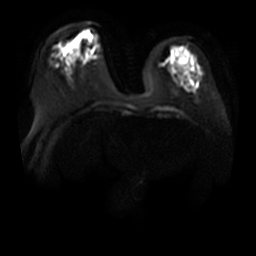
Breast MRI, one axial slice; position 13 of 36 along the scan axis; diffusion-weighted series; image 2 of 4 stored at this slice position (different b-values; order by instance number); 3 T; 256 × 256 image matrix. Female patient.
Outlined on this slice (expert manual segmentation):
- tumour on diffusion-weighted imaging: bounding box <66,43,74,51> (left, top, right, bottom; pixels)